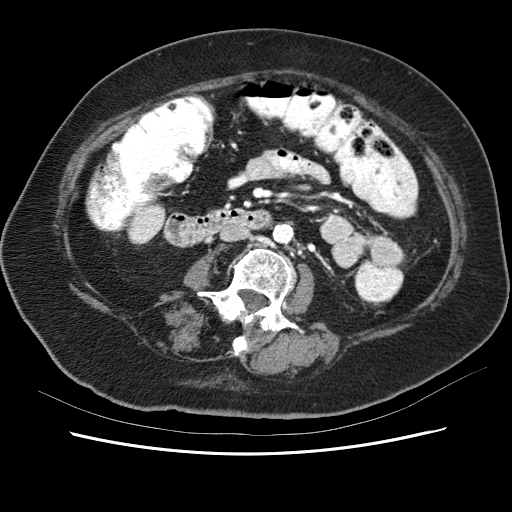
Contrast-enhanced abdominal CT (liver protocol), one axial slice. Slice 5 of 62 in the series (ordered by position). Reconstruction kernel STANDARD. Soft-tissue window (W 400 / L 40 HU). 2.5 mm slice thickness. 512 × 512 image matrix, field of view 340 × 340 mm. Case-level facts recorded for this patient, not image findings: diagnosis: hepatocellular carcinoma (patient treated with transarterial chemoembolisation; whether this scan precedes or follows treatment is not stated here); TNM stage (as recorded): Stage-I; Child-Pugh class: B; tumour nodularity: uninodular; tumour size: 5.3 cm.
Structures marked on this image (semi-automatic segmentation, software-assisted and operator-edited):
- liver parenchyma outside the tumour (the mass and vessels are separate outlines, so this box may not span the whole liver): bounding box <140,196,150,204> (left, top, right, bottom; pixels)
- liver vessels: <142,196,149,201>